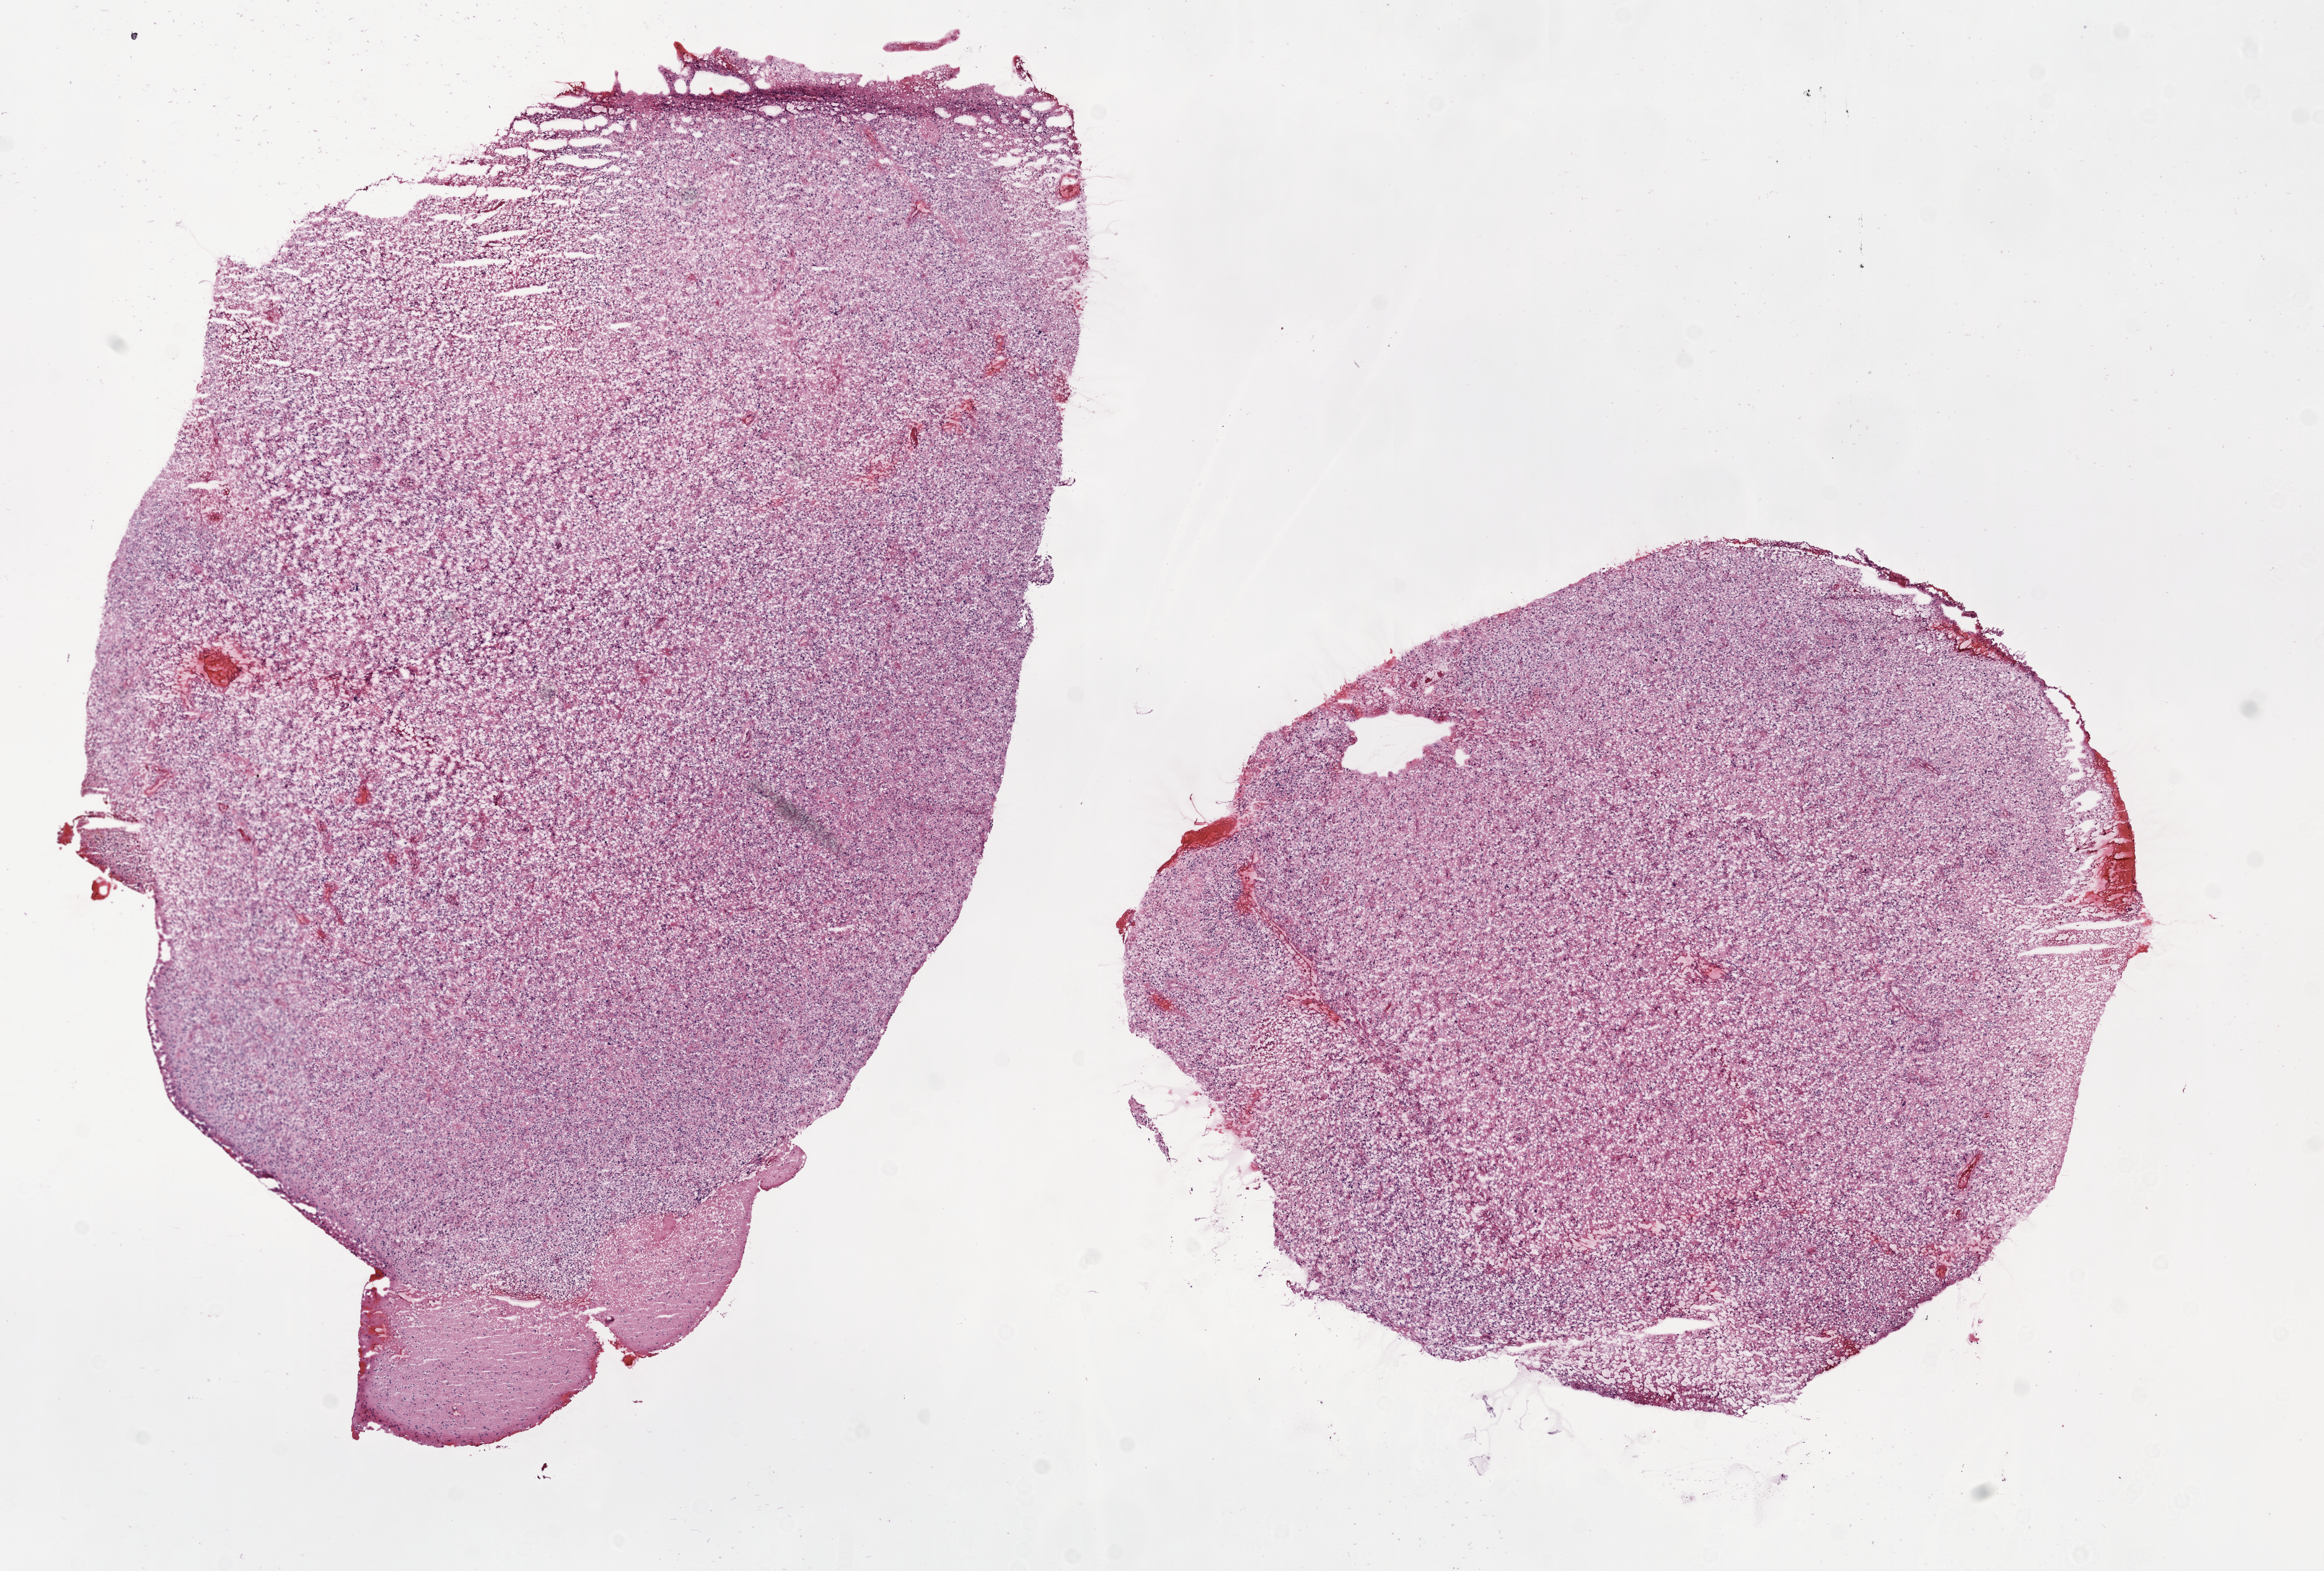
Whole-slide histology image, H&E-stained — shown as a low-resolution overview of the whole scanned area (about 15.0 x 10.2 mm, acquisition: 20x scan), frozen section, primary tumour sample from the brain. Female patient; age at initial diagnosis 66 years. Slide review estimates, as recorded: tumour cells 100%, tumour nuclei 75%, normal cells 0%, stromal cells 0%, necrosis 0%.
- pathologic diagnosis: Glioblastoma